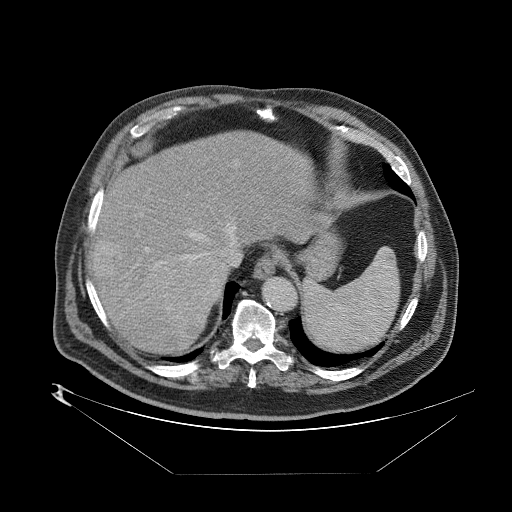
Contrast-enhanced abdominal CT (liver protocol), one axial slice. Position 66 of 89 along the scan axis. 140 kVp. One of 2 acquisitions stored at this slice position. Soft-tissue window (W 400 / L 40 HU). 512 × 512 image matrix, field of view 480 × 480 mm. From the clinical record (not read from this slice): diagnosis: hepatocellular carcinoma (patient treated with transarterial chemoembolisation; whether this scan precedes or follows treatment is not stated here); TNM stage (as recorded): Stage-II; Child-Pugh class: B; tumour nodularity: multinodular; tumour size: 4 cm.
Structures marked on this image (semi-automatically segmented with operator editing):
- abdominal aorta: bounding box [x1, y1, x2, y2] px = [263, 280, 297, 313]
- liver parenchyma outside the tumour (the mass and vessels are separate outlines, so this box may not span the whole liver): [90, 128, 324, 352]
- mass: [153, 248, 226, 323]
- liver vessels: [97, 160, 240, 336]